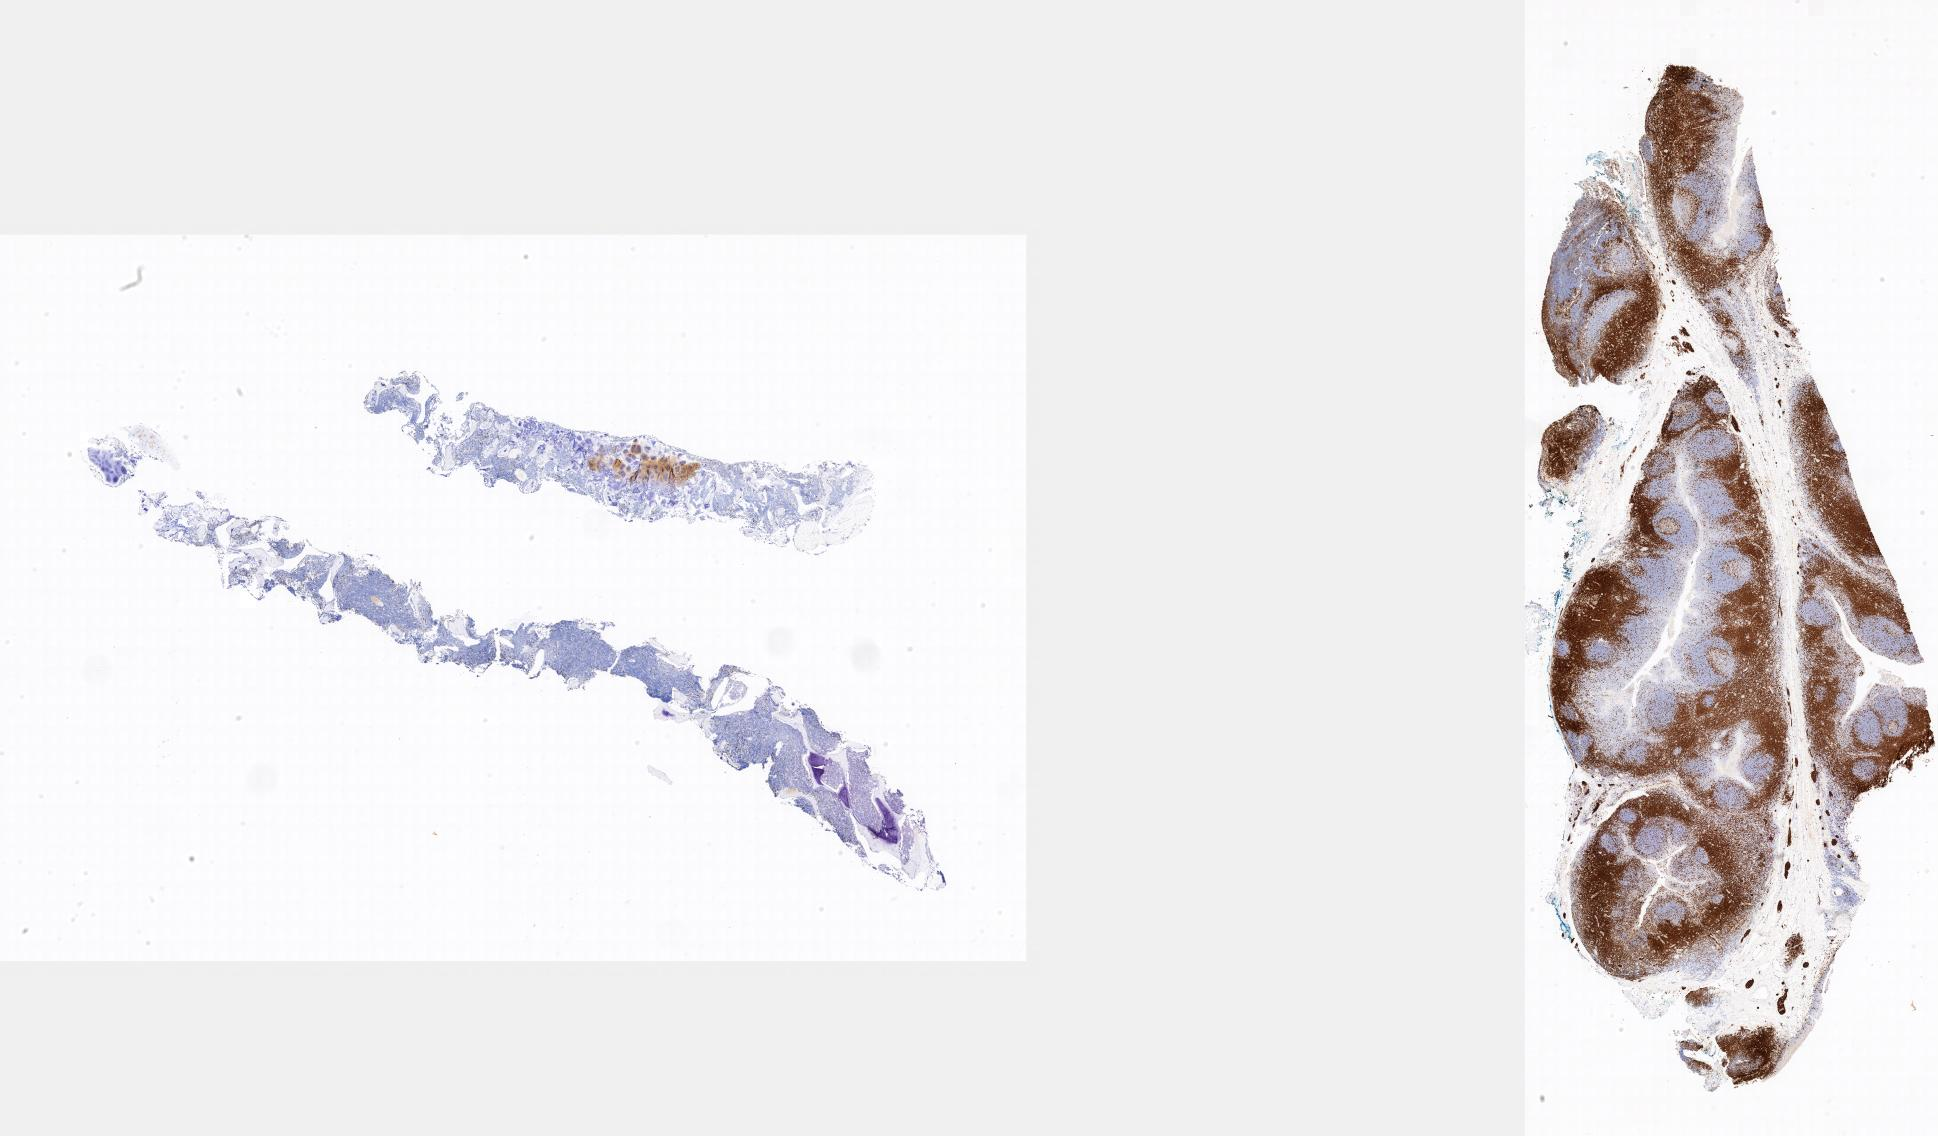
Whole-slide image, immunohistochemical stain for CD3 — low-resolution overview of the scanned area, tumor tissue, anatomic site: bone marrow. Patient male; age 11 years.
- histologic diagnosis: Burkitt lymphoma, NOS